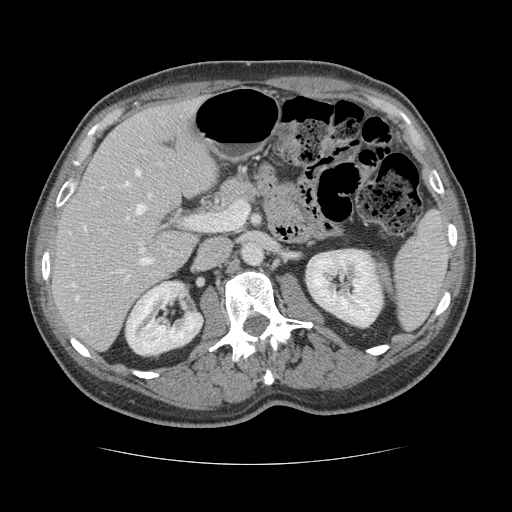
Contrast-enhanced abdominal CT, one axial slice. Slice 71 of 134 in the series (ordered by position). Intravenous contrast given. Soft-tissue window (W 400 / L 40 HU). 2.5 mm slice thickness. 512 × 512 image matrix. Male patient, age 68 years. Case-level facts recorded for this patient, not image findings: diagnosis: colorectal cancer liver metastases, imaged before liver resection; multiple liver metastases: yes; largest metastasis: 2.2 cm; chemotherapy before resection: no.
Structures marked on this image (expert manual segmentation):
- hepatic veins: bounding box [x1, y1, x2, y2] px = [72, 169, 151, 300]
- liver: [53, 100, 217, 349]
- planned liver remnant (the part of the liver to remain after resection): [53, 100, 217, 337]
- portal vein (with intrahepatic branches): [120, 216, 152, 279]